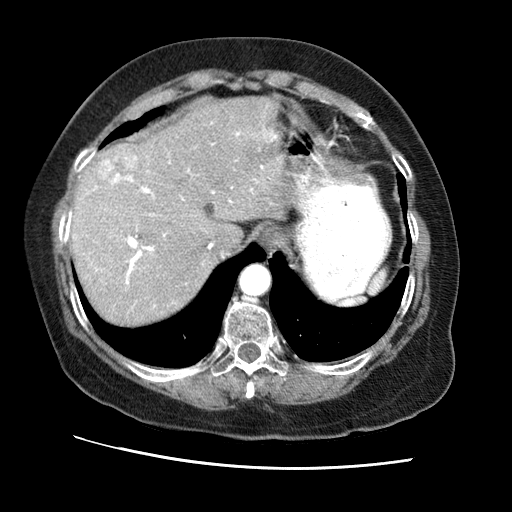
Contrast-enhanced abdominal CT (liver protocol), one axial slice. Position 52 of 65 along the scan axis. Reconstruction kernel STANDARD. Soft-tissue window (W 400 / L 40 HU). 2.5 mm slice thickness. 512 × 512 image matrix, field of view 340 × 340 mm. Case-level facts recorded for this patient, not image findings: diagnosis: hepatocellular carcinoma (patient treated with transarterial chemoembolisation; whether this scan precedes or follows treatment is not stated here); TNM stage (as recorded): Stage-II; Child-Pugh class: A; tumour differentiation: no biopsy; tumour nodularity: multinodular.
Annotated regions visible in this slice (semi-automatically segmented with operator editing):
- abdominal aorta: bounding box (x1, y1, x2, y2) in pixels: (241, 265, 270, 294)
- liver parenchyma outside the tumour (the mass and vessels are separate outlines, so this box may not span the whole liver): (68, 96, 287, 324)
- mass: (94, 144, 139, 186)
- liver vessels: (68, 132, 277, 307)